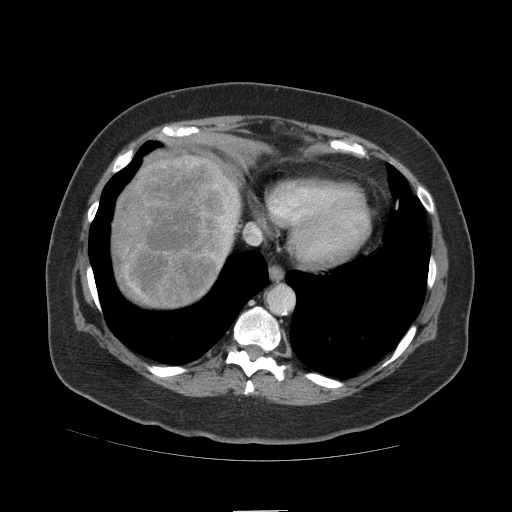
Contrast-enhanced abdominal CT (liver protocol), one axial slice. Position 95 of 109 along the scan axis. Soft-tissue window (W 400 / L 40 HU). 512 × 512 image matrix, field of view 420 × 420 mm. From the clinical record (not read from this slice): diagnosis: hepatocellular carcinoma (patient treated with transarterial chemoembolisation; whether this scan precedes or follows treatment is not stated here); TNM stage (as recorded): Stage-IVB; Child-Pugh class: A; tumour nodularity: multinodular.
Structures marked on this image (semi-automatically segmented with operator editing):
- liver parenchyma outside the tumour (the mass and vessels are separate outlines, so this box may not span the whole liver): box from (x=110, y=152) to (x=240, y=308) px
- mass: (x=112, y=152)–(x=239, y=306)